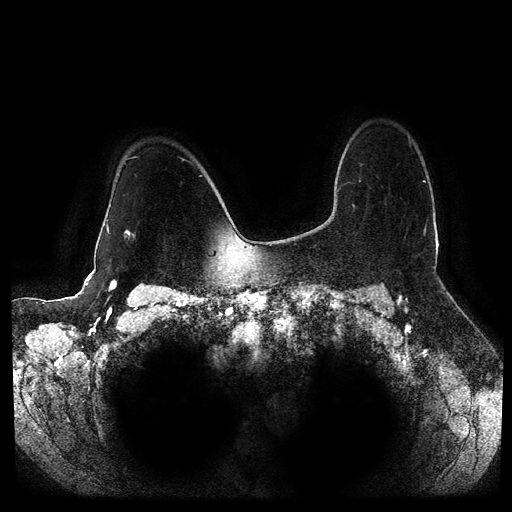
Breast MRI (dynamic contrast-enhanced, multi-phase), one axial slice; dynamic contrast-enhanced series, time point 2 of 5 at this slice position (early post-contrast); 1.5 T; TE 2.6 ms, TR 5.2 ms; 2 mm slice thickness; 512 × 512 image matrix, field of view 380 × 380 mm. Female patient, age 53 years.
Outlined on this slice (semi-automatic segmentation, software-assisted and operator-edited):
- breast lesion (labelled 'tumour' in the annotation; benign lesions carry a separate 'benign' label): bounding box (x1, y1, x2, y2) in pixels: (124, 230, 133, 239)